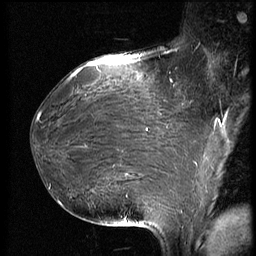
Breast MRI (dynamic contrast-enhanced), one sagittal slice; position 30 of 66 along the scan axis; dynamic contrast-enhanced series, image 2 of 3 at this slice position (ordered by acquisition); 1.5 T; TE 4.2 ms, TR 8.9 ms; 2.5 mm slice thickness; 256 × 256 image matrix, field of view 200 × 200 mm. Patient: female, 39 years. From the clinical record (not read from this slice): setting: breast cancer imaged before/during neoadjuvant chemotherapy; receptor status: HER2-positive.
Structures marked on this image (semi-automatically segmented with operator editing):
- analysis volume of interest (the breast-tissue region the enhancement analysis was run in; not a lesion): bounding box [x1, y1, x2, y2] px = [32, 75, 188, 218]
- tumour enhancement mask (voxels above the 140 % enhancement threshold inside the analysis volume of interest): [37, 75, 147, 131]